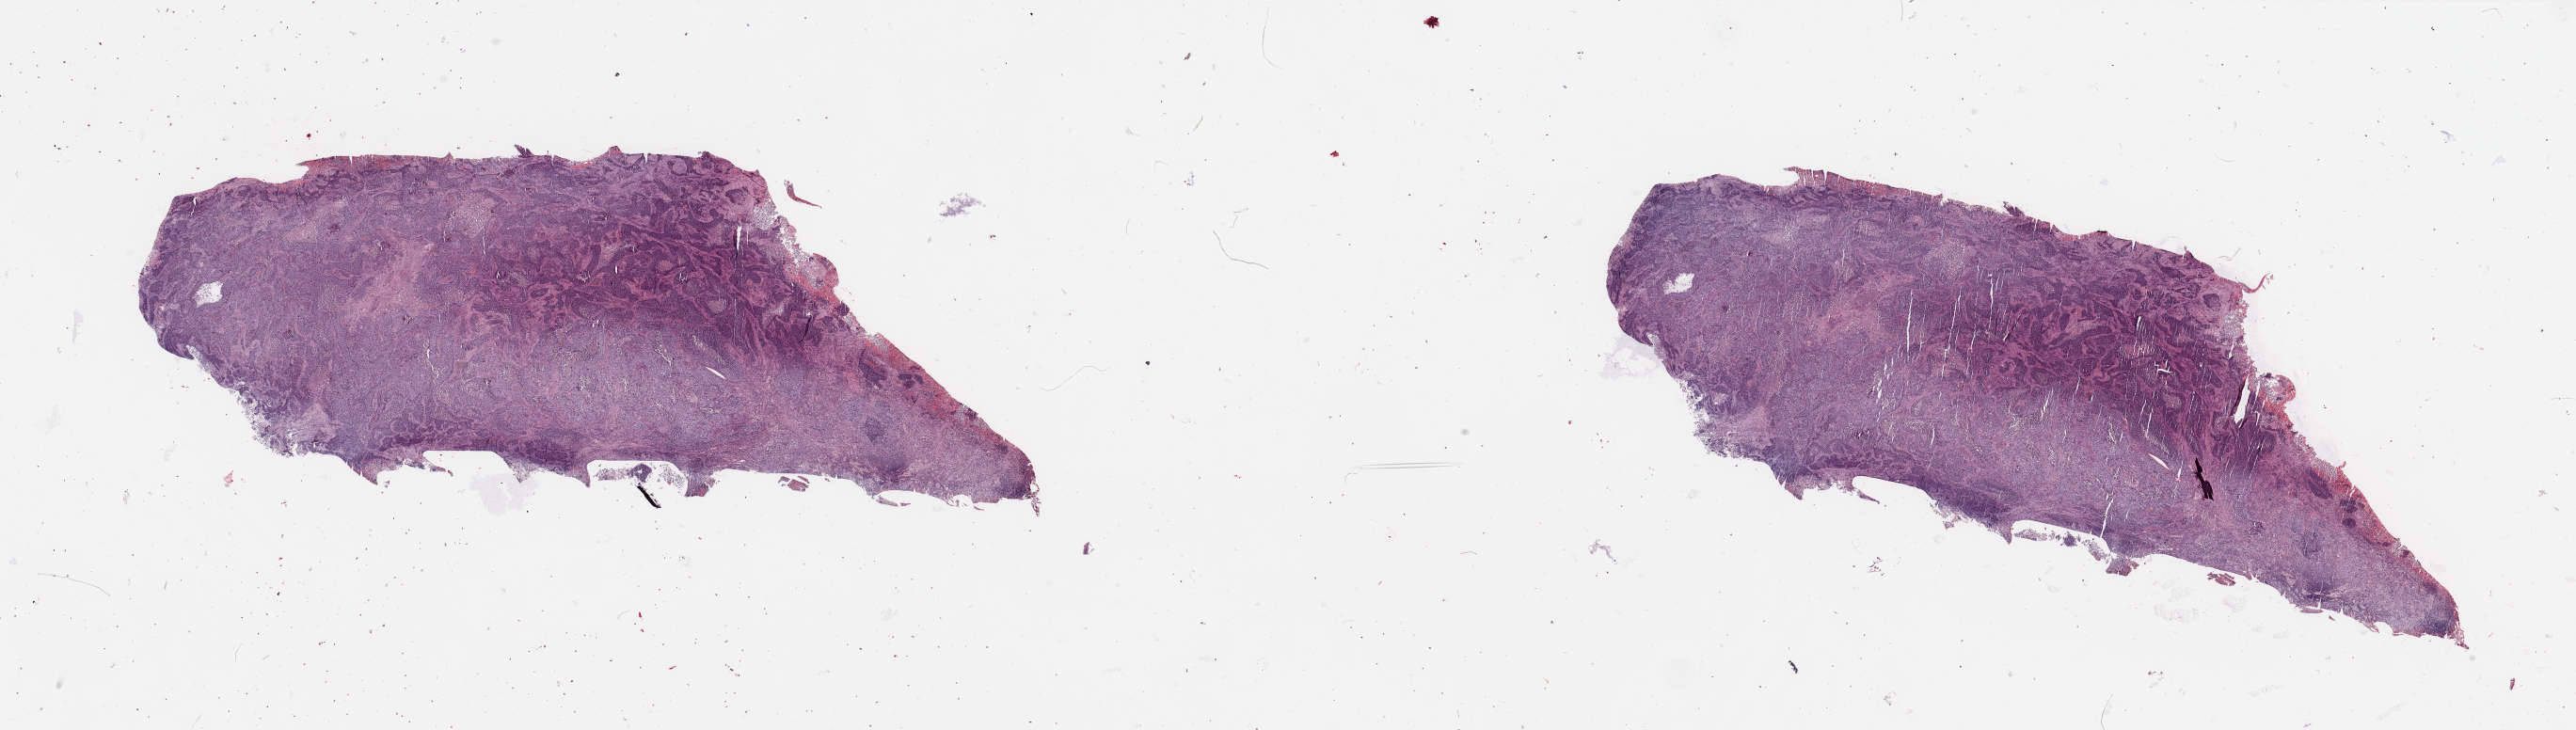
Hematoxylin and eosin (H&E) stained whole-slide image, low-resolution overview of the scanned area, about 43.3 x 12.3 mm (slide scanned at 20x). Tumour tissue sample, sampled site: lung. Male, 73 y/o. Histologic grade: G3 (poorly differentiated). Pathologist review of this section (percent, as recorded): tumour nuclei 65%, necrosis 15%.
Diagnosis: Squamous cell carcinoma, NOS. AJCC pathologic stage: IIB. Primary tumour site (as recorded): left upper lobe.